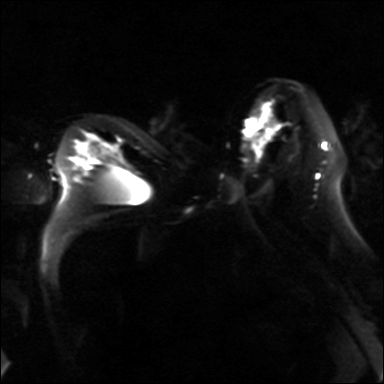
Breast MRI, one axial slice; slice 19 of 36 in the series (ordered by position); diffusion-weighted series; image 2 of 4 stored at this slice position (different b-values; order by instance number); 3 T; 384 × 384 image matrix, field of view 320 × 320 mm. Female patient.
Annotated regions visible in this slice (outlined manually by an expert reader):
- tumour on diffusion-weighted imaging: bounding box <255,110,275,138> (left, top, right, bottom; pixels)